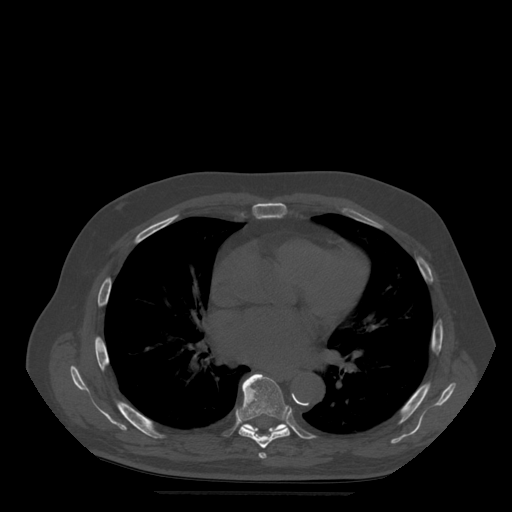
CT including the spine, one axial slice. Position 328 of 522 along the scan axis. Bone window (W 1800 / L 400 HU). 512 × 512 image matrix. Patient age 72 years. From the clinical record (not read from this slice): primary cancer: prostate.
Annotated regions visible in this slice (semi-automatically segmented with operator editing):
- T6 vertebra: bounding box (x1, y1, x2, y2) in pixels: (259, 453, 267, 459)
- T7 vertebra: (237, 374, 290, 449)
- T8 vertebra: (244, 424, 288, 432)